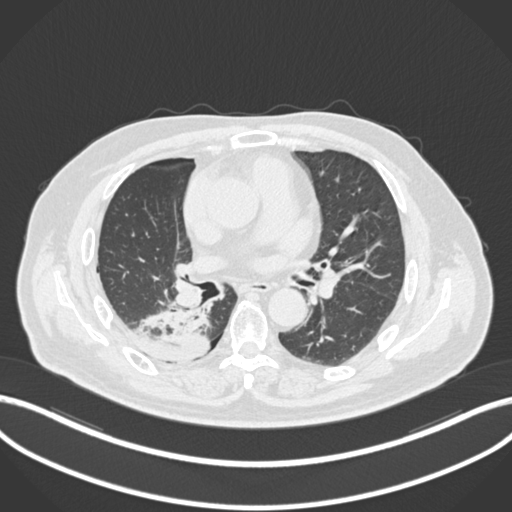
Chest CT, one axial slice. Position 98 of 218 along the scan axis. 120 kVp. Lung window (W 1500 / L -600 HU). 1 mm slice thickness. 512 × 512 image matrix, field of view 400 × 400 mm. Male patient, age 68 years. From the clinical record (not read from this slice): clinical TNM (as recorded): T2a N0 M0.
Outlined on this slice (rectangle marked by the reading radiologist):
- lung tumour (recorded histology: adenocarcinoma): bounding box <133,296,212,362> (left, top, right, bottom; pixels)